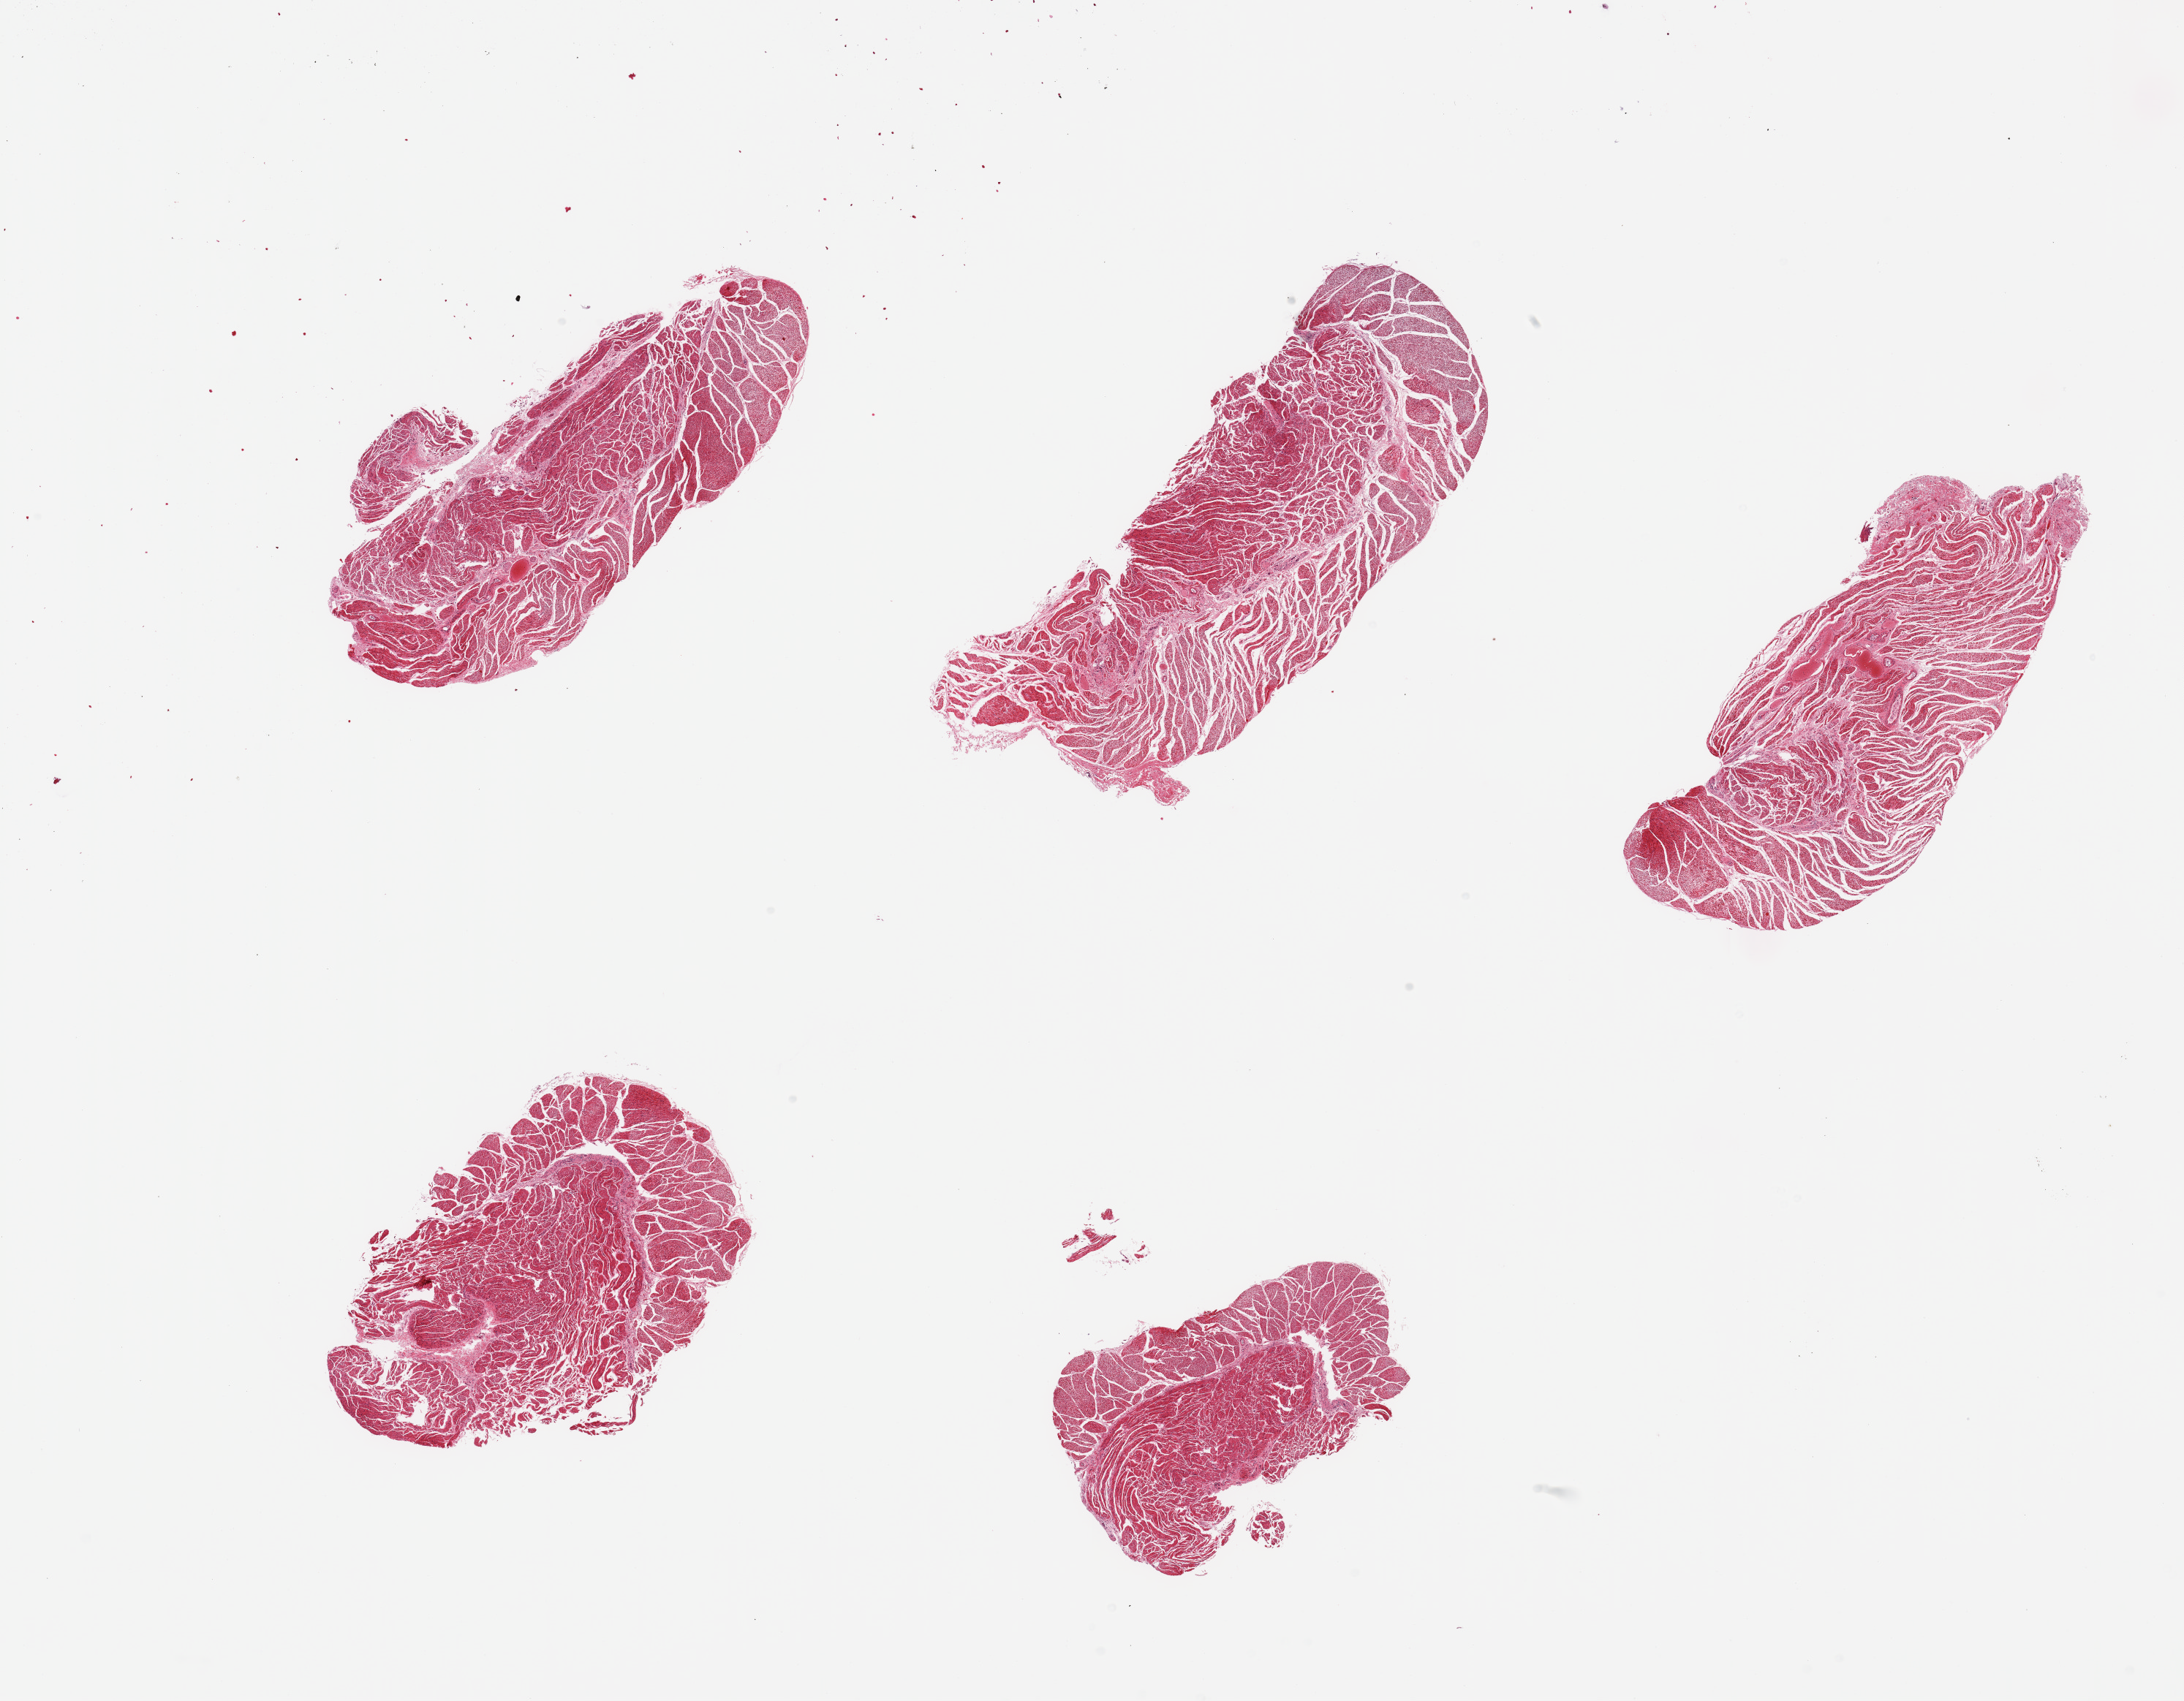
H&E whole-slide image, brightfield — low-resolution overview of the scanned area, about 23.6 x 18.4 mm (slide scanned at 20x). PAXgene-fixed paraffin-embedded (PFPE) section. Section of esophageal muscle (target tissue). Donor tissue sample. Male donor.
Review note (as recorded): 5 pieces, confirmed target muscularis.